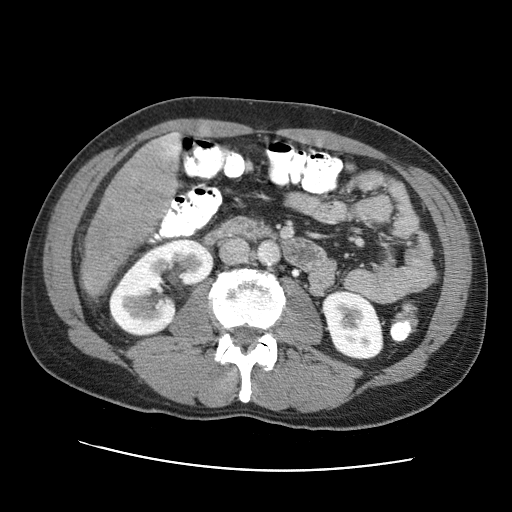
Contrast-enhanced abdominal CT (liver protocol), one axial slice; slice 16 of 95 in the series (ordered by position); 120 kVp; one of 2 acquisitions stored at this slice position; soft-tissue window (W 400 / L 40 HU); 512 × 512 image matrix, field of view 360 × 360 mm. From the clinical record (not read from this slice): diagnosis: hepatocellular carcinoma (patient treated with transarterial chemoembolisation; whether this scan precedes or follows treatment is not stated here); TNM stage (as recorded): Stage-IVA; Child-Pugh class: A; tumour differentiation: moderately differentiated; tumour nodularity: multinodular.
Structures marked on this image (semi-automatically segmented with operator editing):
- liver parenchyma outside the tumour (the mass and vessels are separate outlines, so this box may not span the whole liver): box from (x=150, y=132) to (x=180, y=238) px
- mass: (x=79, y=132)–(x=177, y=298)
- liver vessels: (x=175, y=133)–(x=180, y=155)